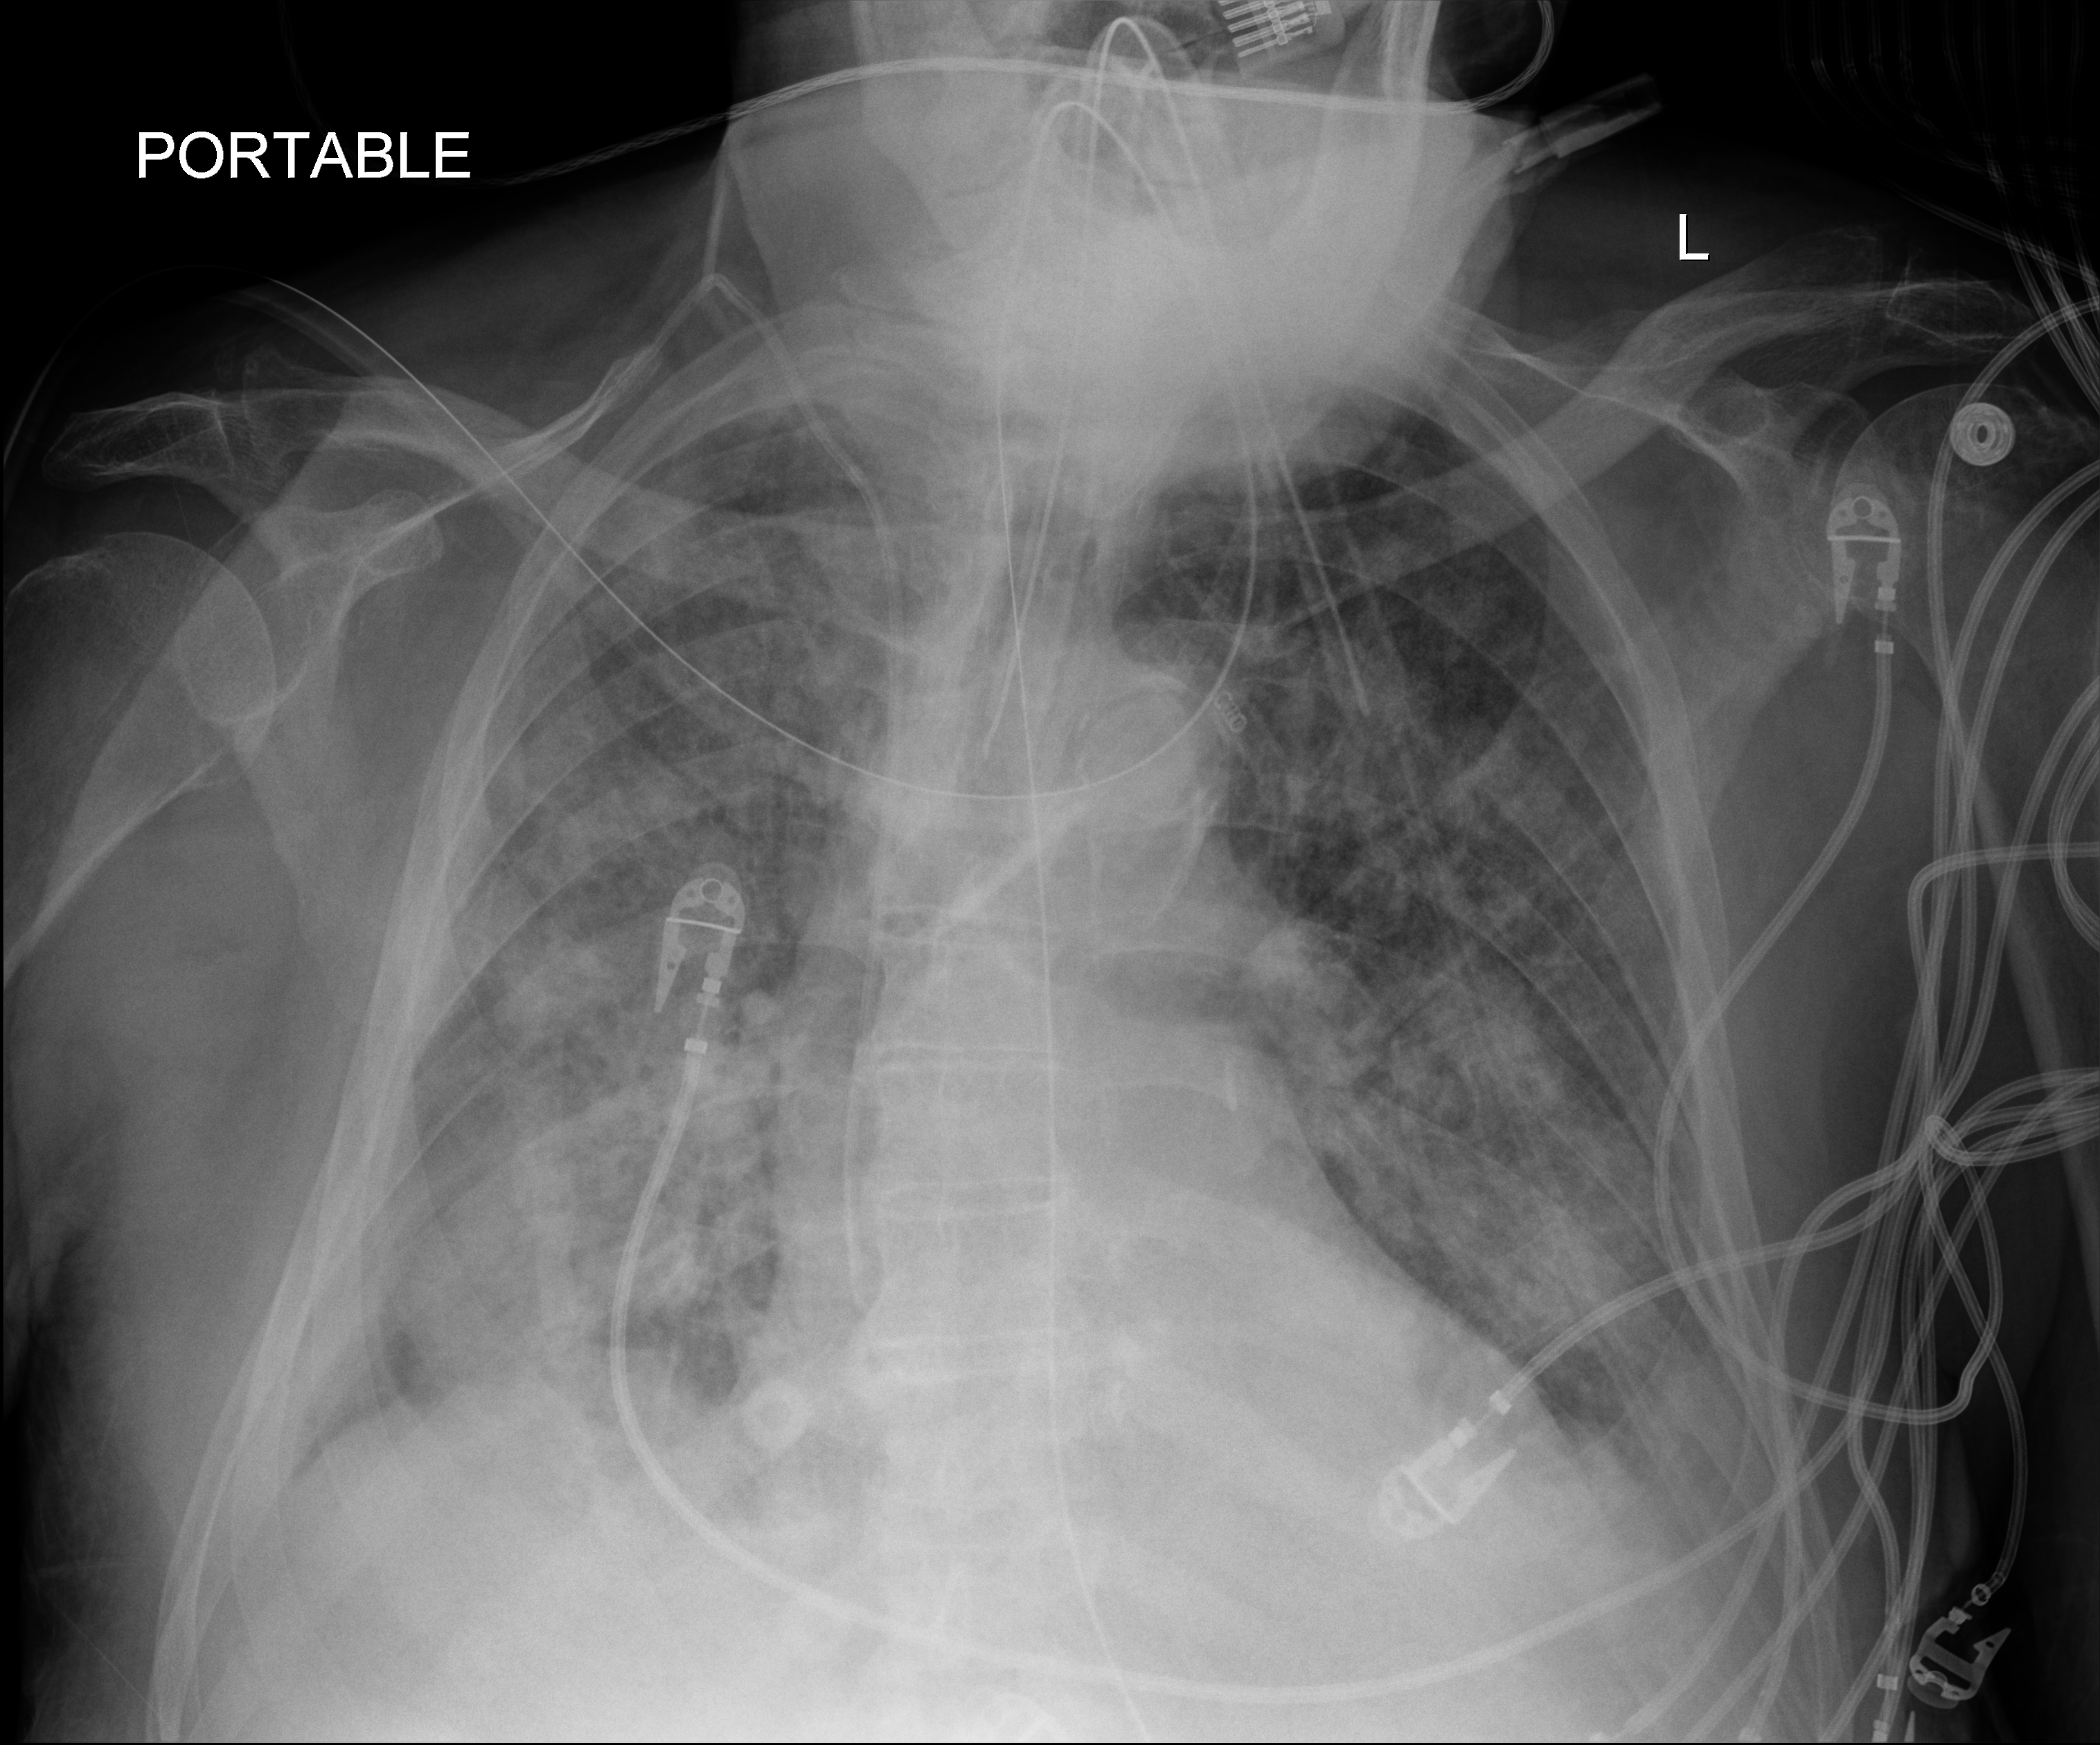
Portable chest radiograph. Patient hospitalised with COVID-19; male, aged 75–90 years.
From the hospital-stay record, not from the radiograph (when in the stay this image was taken is not recorded): hypertension (admission record): yes; diabetes (admission record): yes; length of hospital stay: 28 days.